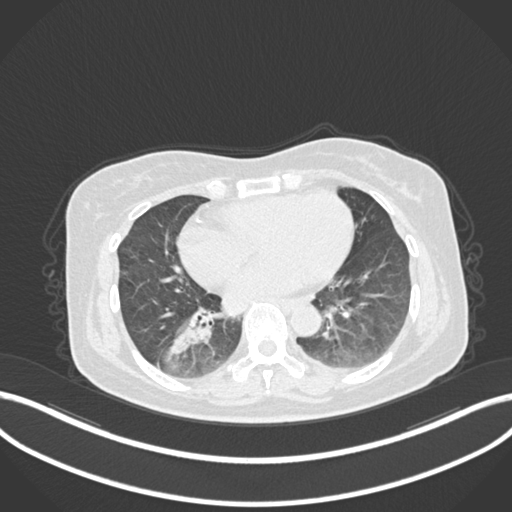
Chest CT, one axial slice. Slice 57 of 222 in the series (ordered by position). Reconstruction kernel B30f. Lung window (W 1500 / L -600 HU). 1 mm slice thickness. 512 × 512 image matrix. Patient: female, 67 years. From the clinical record (not read from this slice): clinical TNM (as recorded): T1c N1 M0; histopathological grade: G2-3.
Structures marked on this image (bounding box drawn by a radiologist):
- lung tumour (recorded histology: adenocarcinoma): bounding box (x1, y1, x2, y2) in pixels: (161, 301, 215, 364)